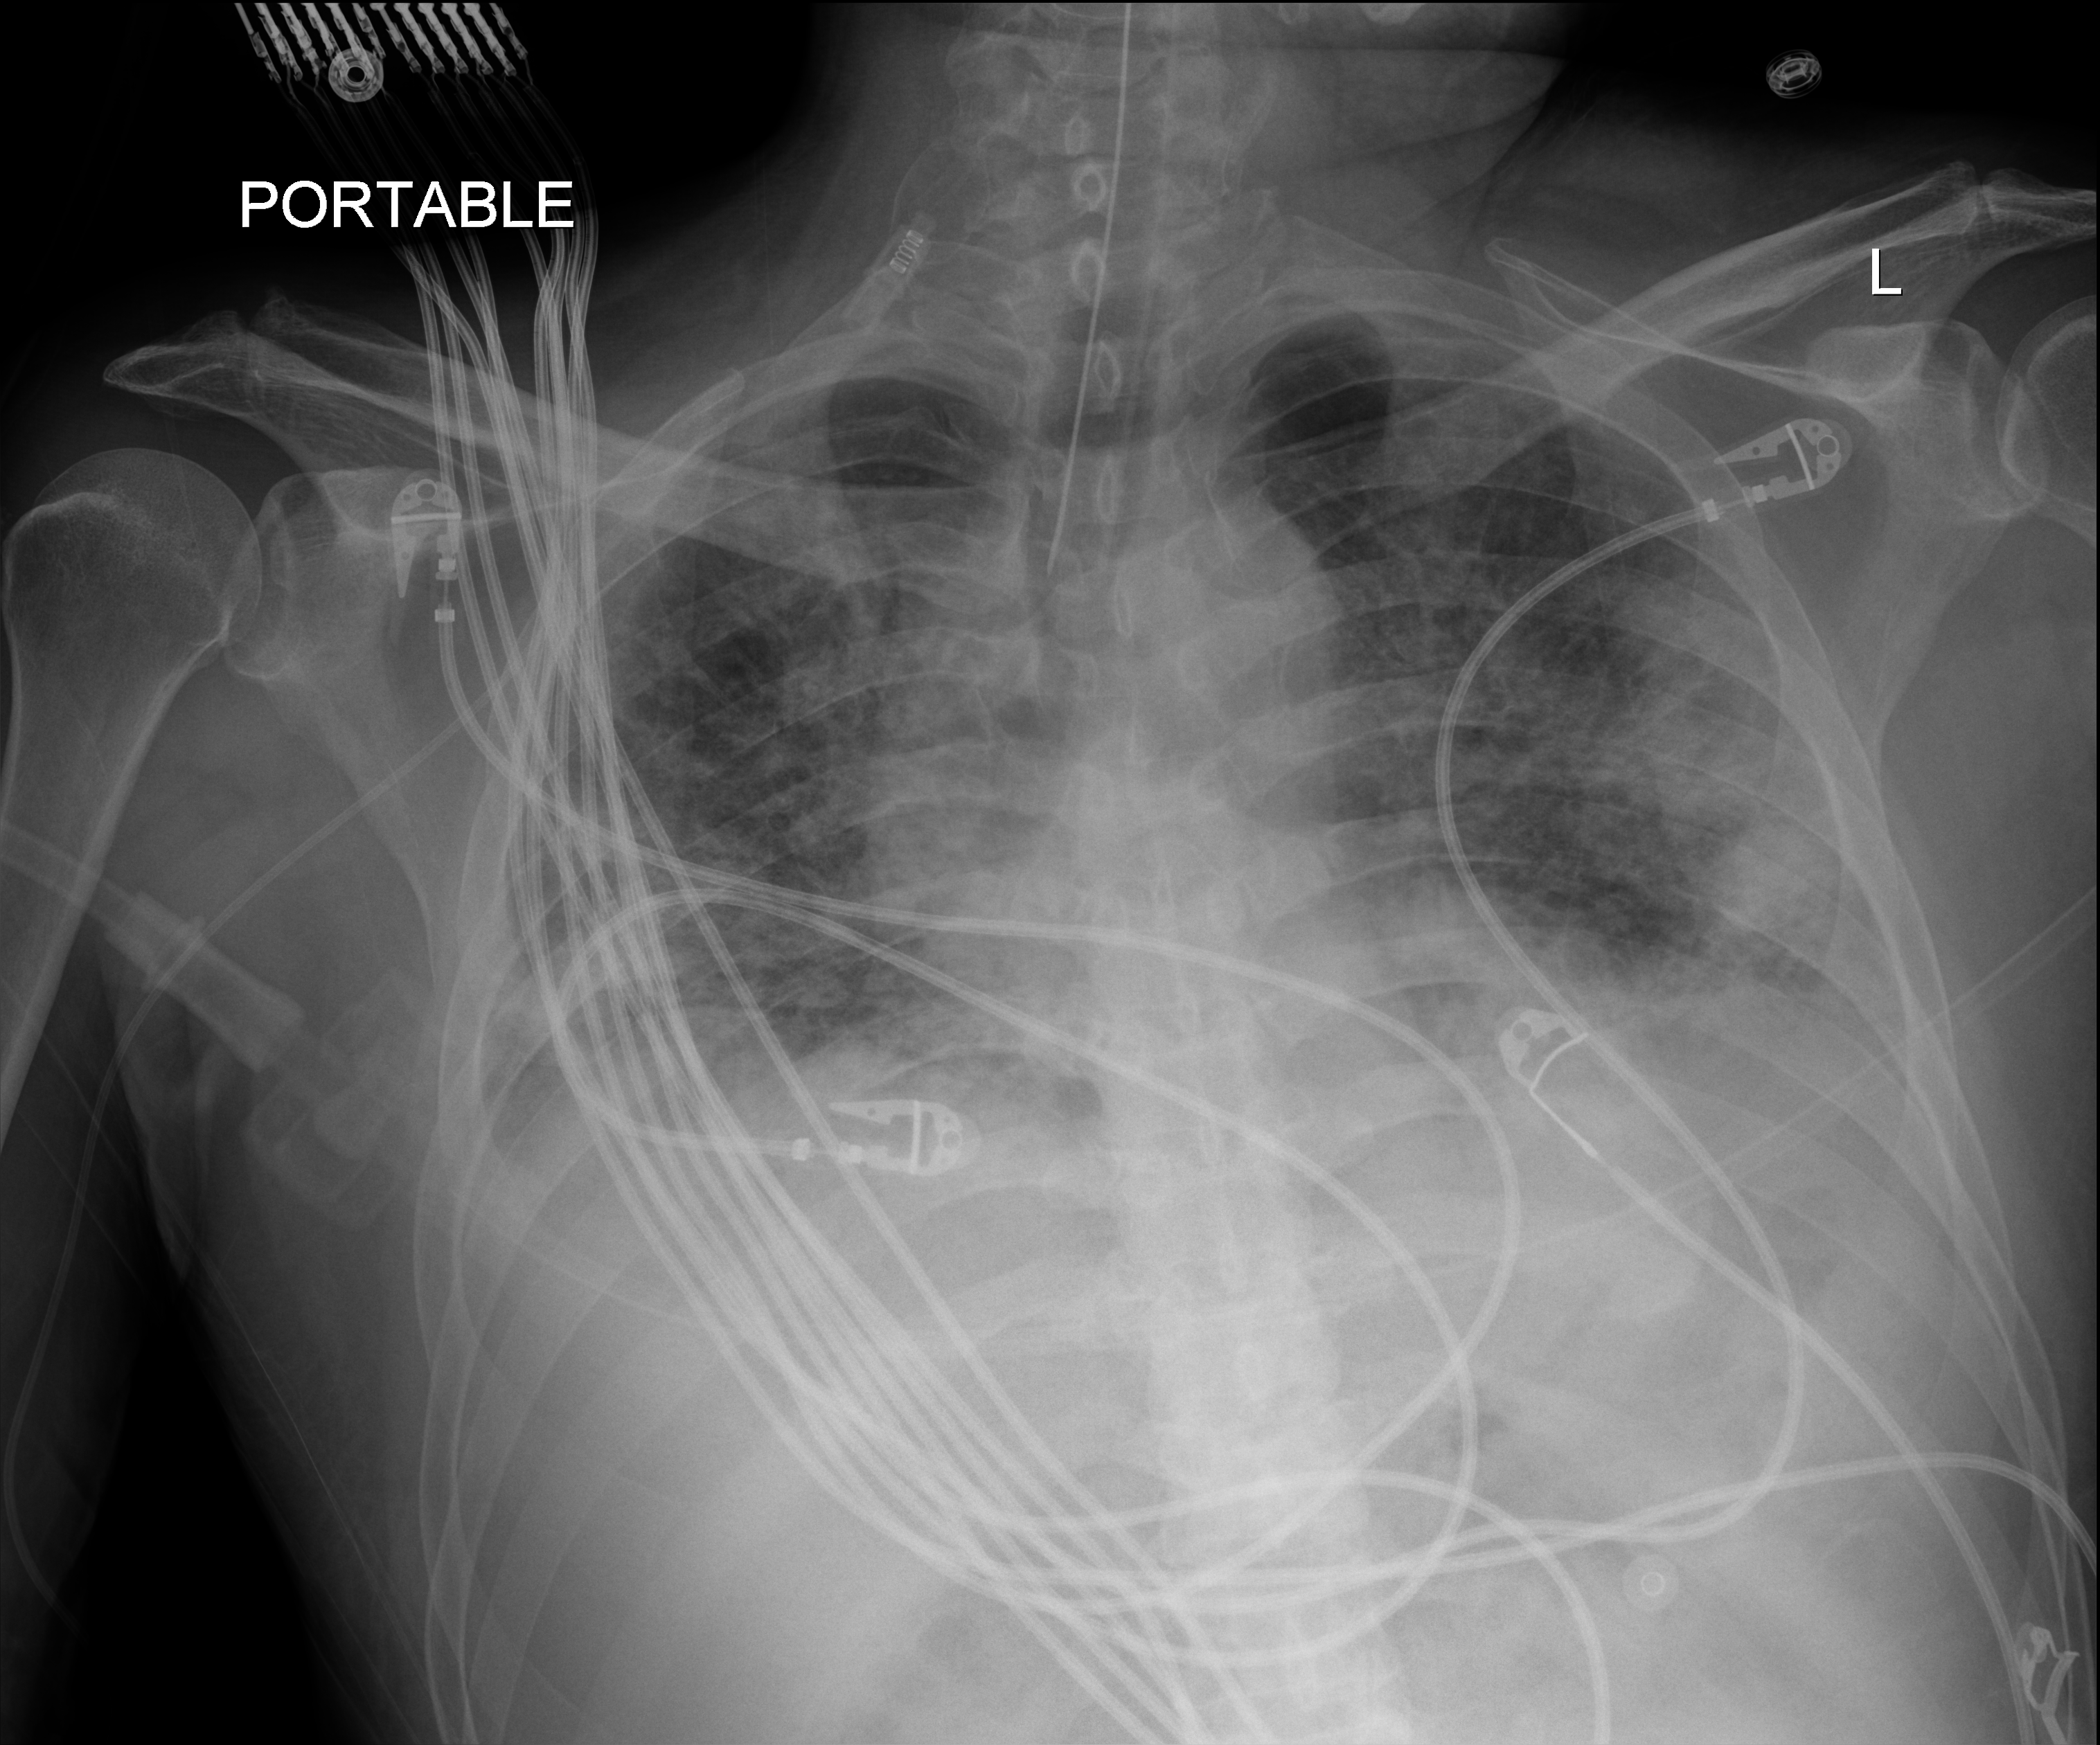
Portable chest radiograph. Patient hospitalised with COVID-19; male, aged 18–59 years.
Hospital-stay facts (about this admission, not read from this image; timing relative to this image not recorded):
- chronic kidney disease (admission record): no
- length of hospital stay: 40 days
- admitted to intensive care during this hospital stay: yes